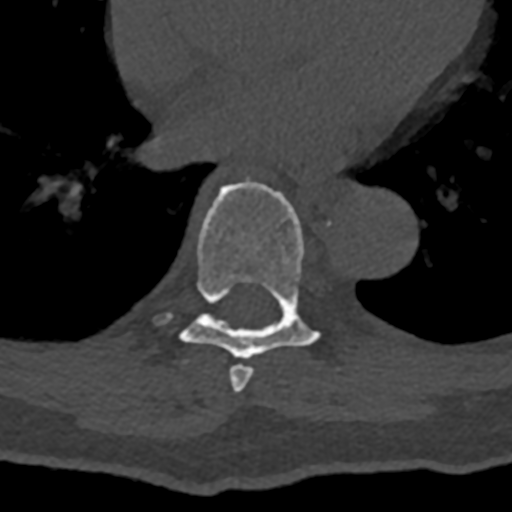
CT including the spine, one axial slice. 120 kVp. Bone window (W 1800 / L 400 HU). 0.5 mm slice thickness. 512 × 512 image matrix, field of view 160 × 160 mm. Male patient, age 74 years. From the clinical record (not read from this slice): primary cancer: renal.
Structures marked on this image (semi-automatically segmented with operator editing):
- T7 vertebra: bounding box [x1, y1, x2, y2] px = [229, 365, 253, 393]
- T8 vertebra: [156, 180, 330, 359]